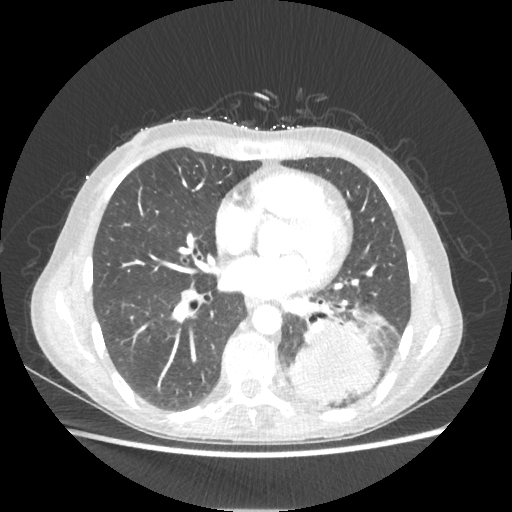
Chest CT, one axial slice; position 99 of 221 along the scan axis; lung window (W 1500 / L -600 HU); 1.25 mm slice thickness; 512 × 512 image matrix, field of view 360 × 360 mm. Patient: female, 53 years. From the clinical record (not read from this slice): clinical TNM (as recorded): T3 N0 M0.
Structures marked on this image (bounding box drawn by a radiologist):
- lung tumour (recorded histology: adenocarcinoma): bounding box (x1, y1, x2, y2) in pixels: (287, 322, 379, 407)